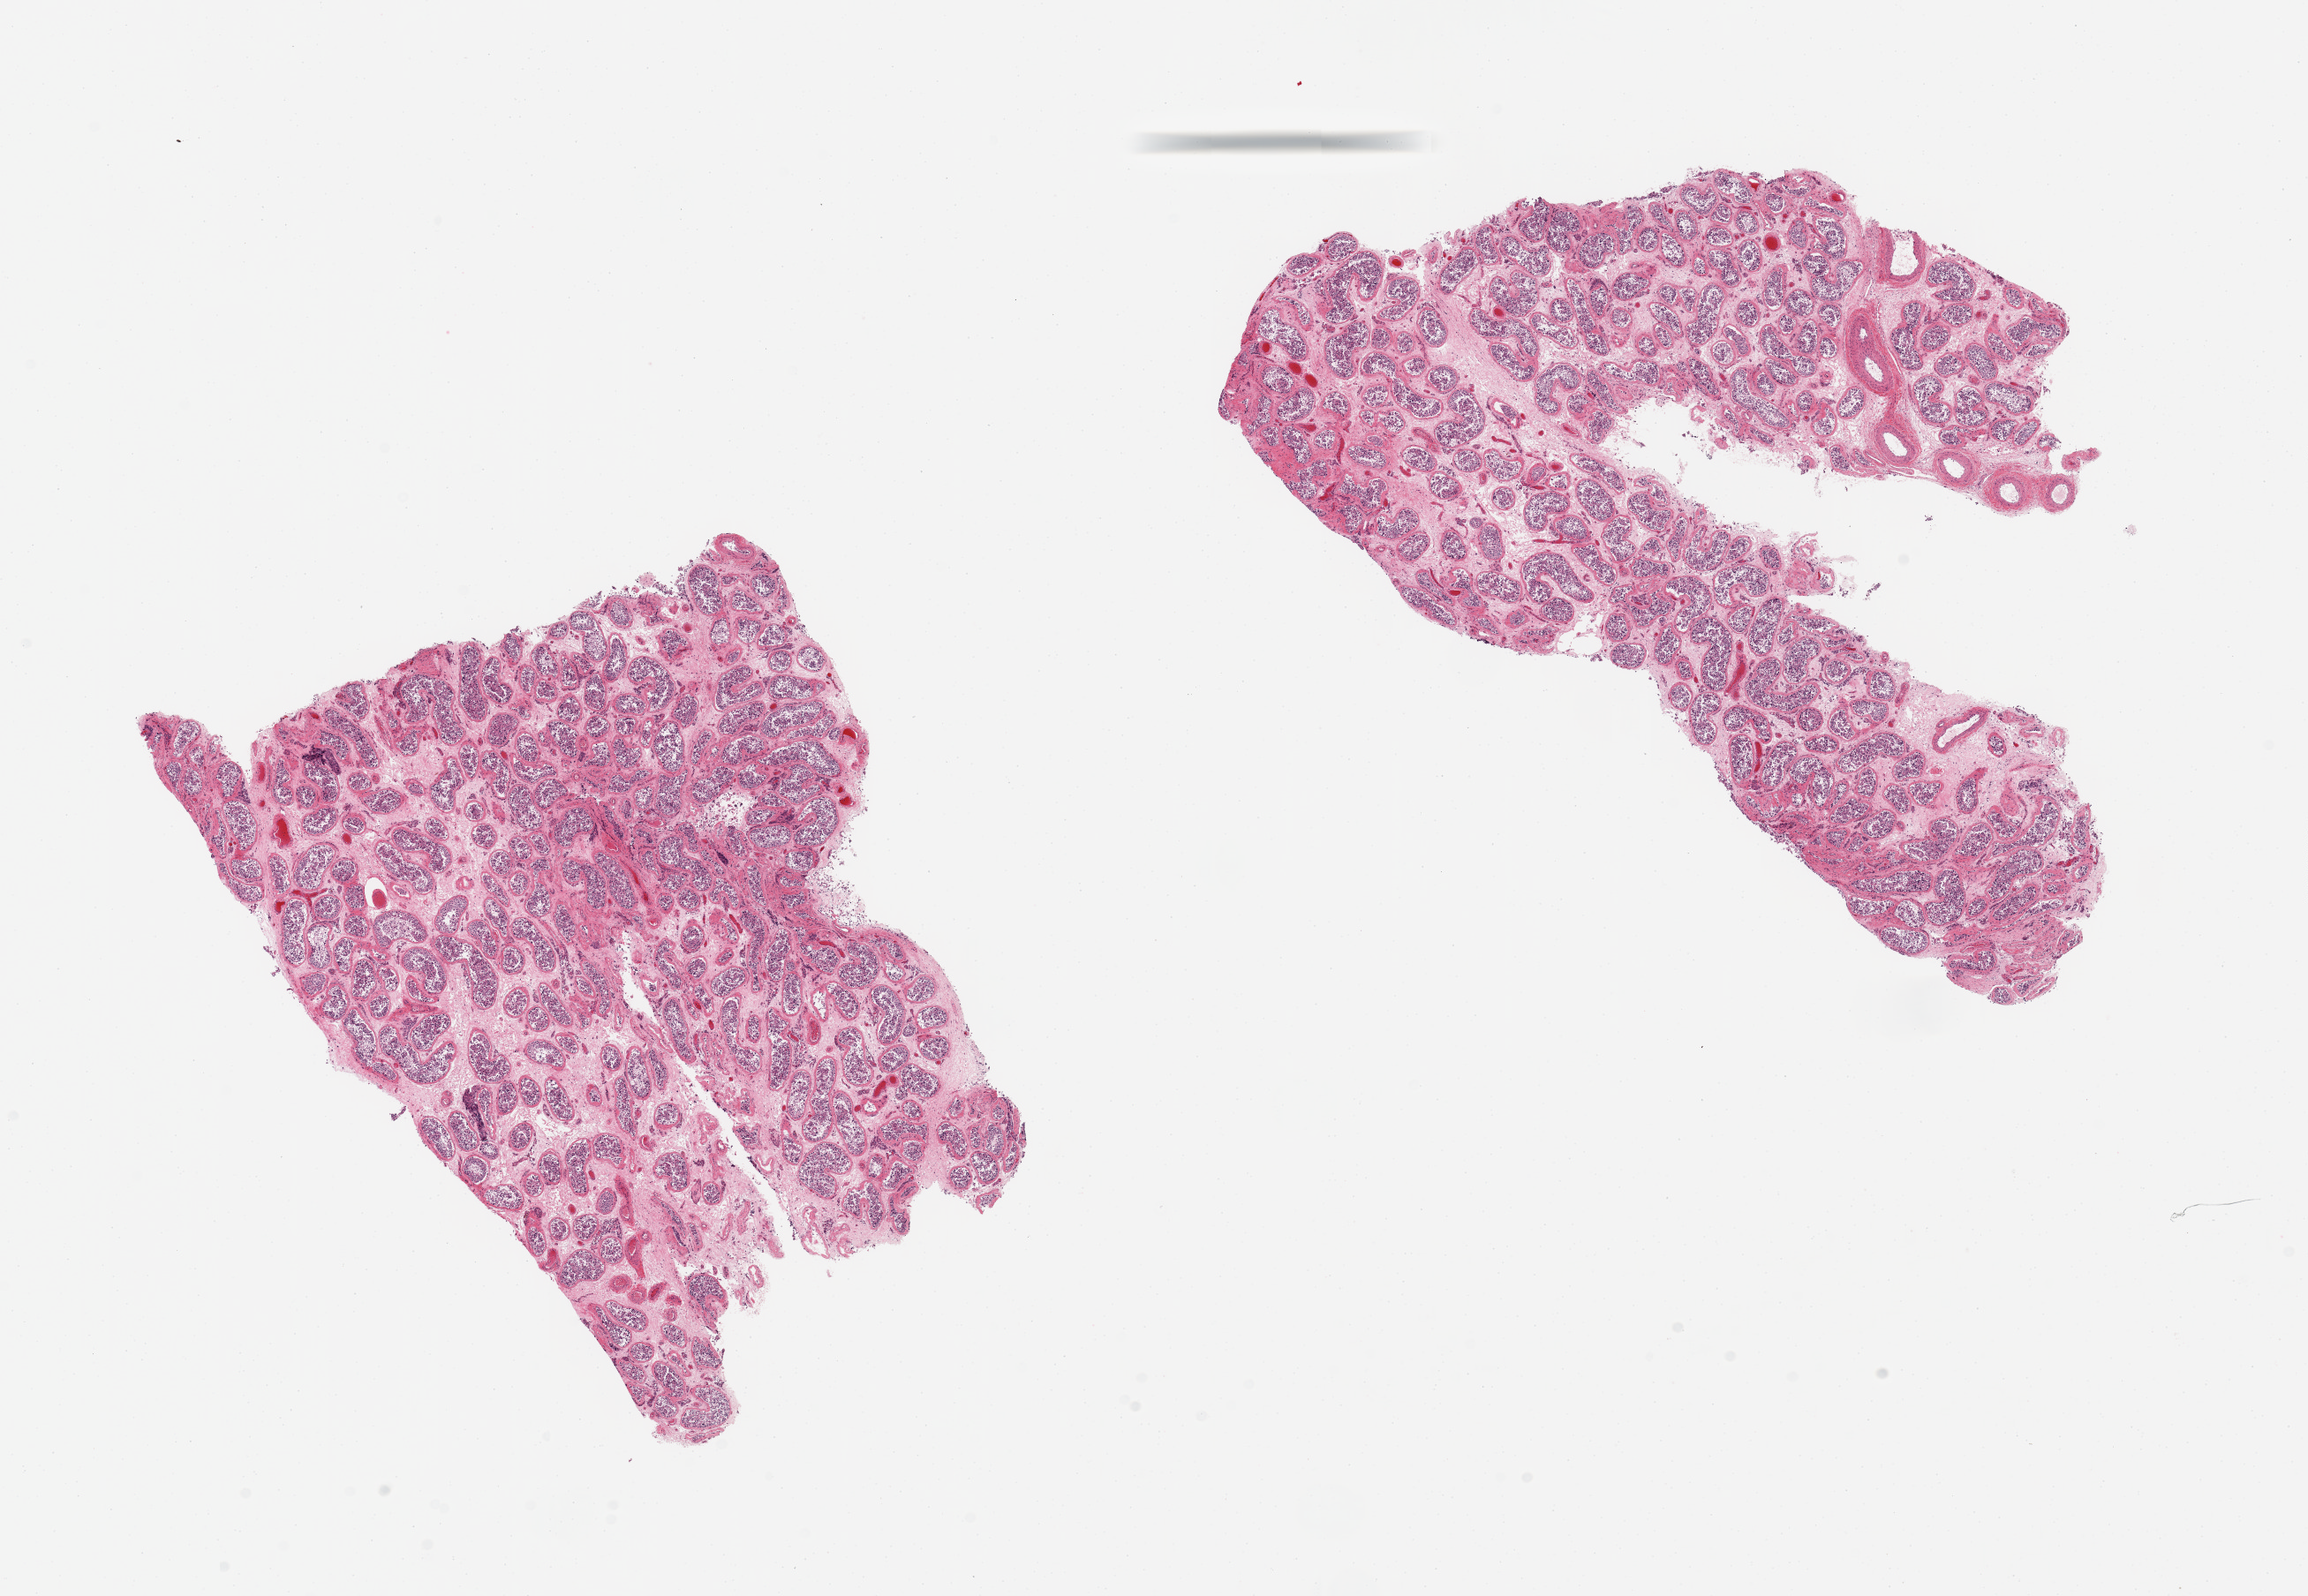
Hematoxylin and eosin (H&E) whole-slide image, whole scanned area (about 20.7 x 14.3 mm) shown as a low-resolution overview. PAXgene-fixed paraffin-embedded (PFPE) section. Target tissue: testis. Tissue donor sample. Donor: male.
Reviewer comment on this tissue sample: 2 pieces; spermatogenesis is present, increased peritubular fibrosis.